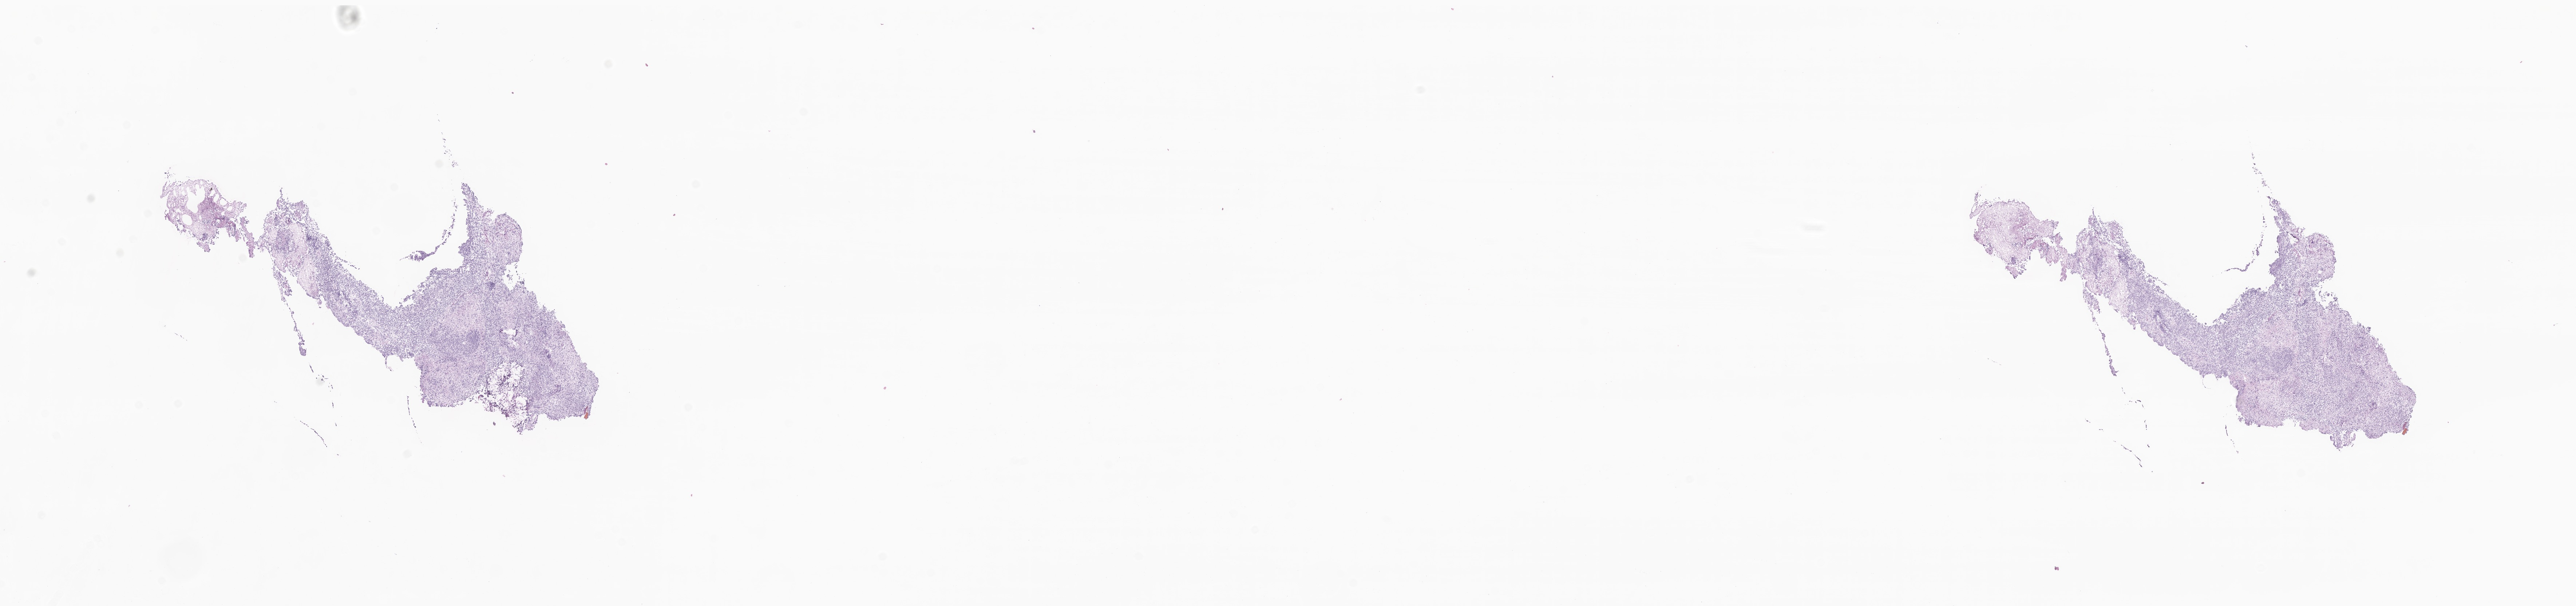
Digitized haematoxylin and eosin-stained section of tumor tissue from the cerebellum — low-resolution overview of the scanned area, about 29.8 x 7.0 mm; frozen section (OCT-embedded). Male patient, age 165 months (13 years 9 months).
• diagnosis (ICD-O-3 morphology term): Medulloblastoma, NOS